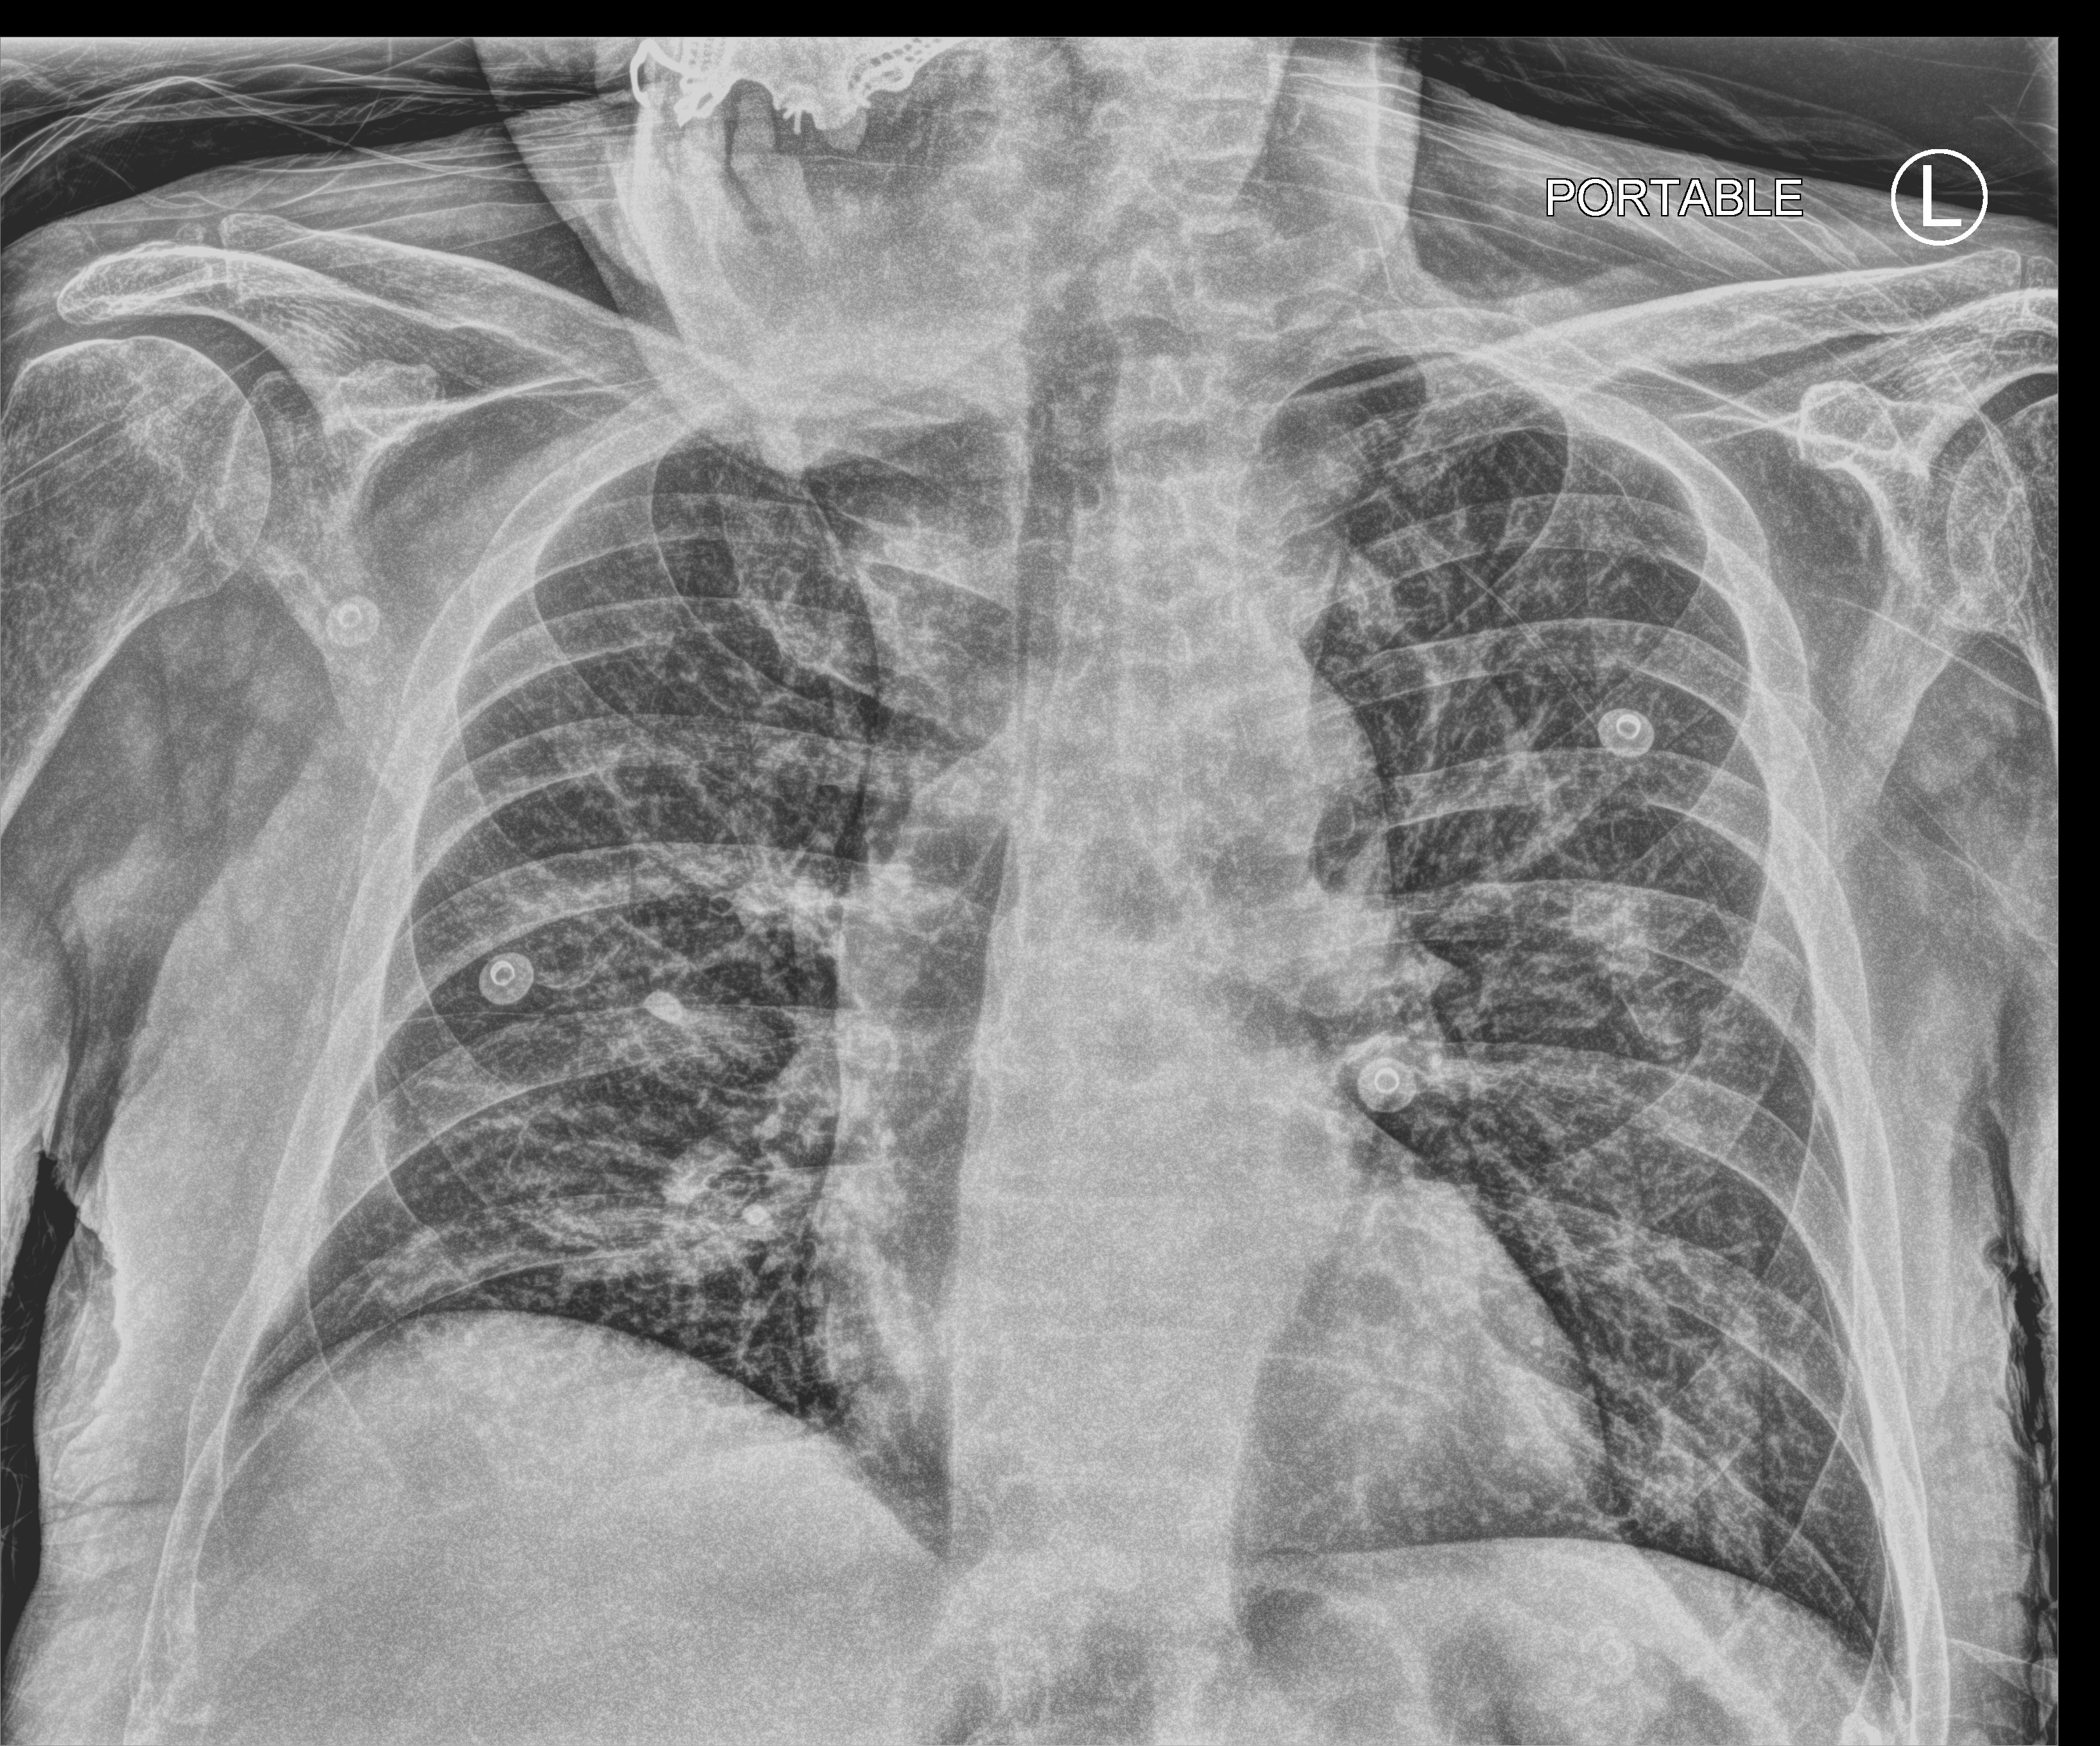
Bedside chest radiograph (computed radiography); anteroposterior (AP) projection. Male patient hospitalised with COVID-19, age 60–74 years.
Admission-level facts for this patient (not findings on this image; timing relative to this image not recorded): chronic kidney disease (admission record): no.